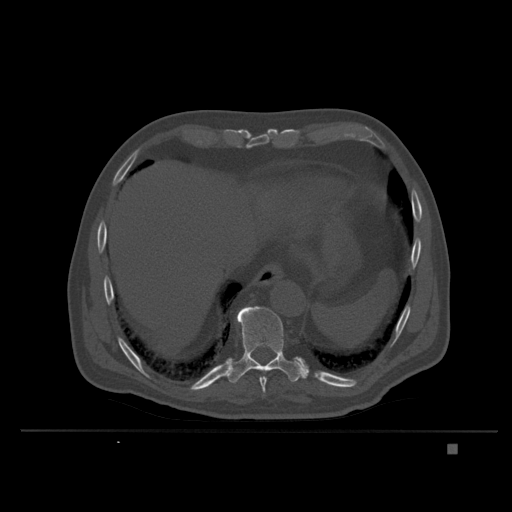
CT including the spine, one axial slice; position 198 of 435 along the scan axis; bone window (W 1800 / L 400 HU); 1.5 mm slice thickness; 512 × 512 image matrix, field of view 434 × 434 mm. Patient: male, 73 years. From the clinical record (not read from this slice): primary cancer: skin.
Structures marked on this image (semi-automatically segmented with operator editing):
- T10 vertebra: box from (x=228, y=305) to (x=306, y=384) px
- T9 vertebra: (x=259, y=370)–(x=269, y=397)